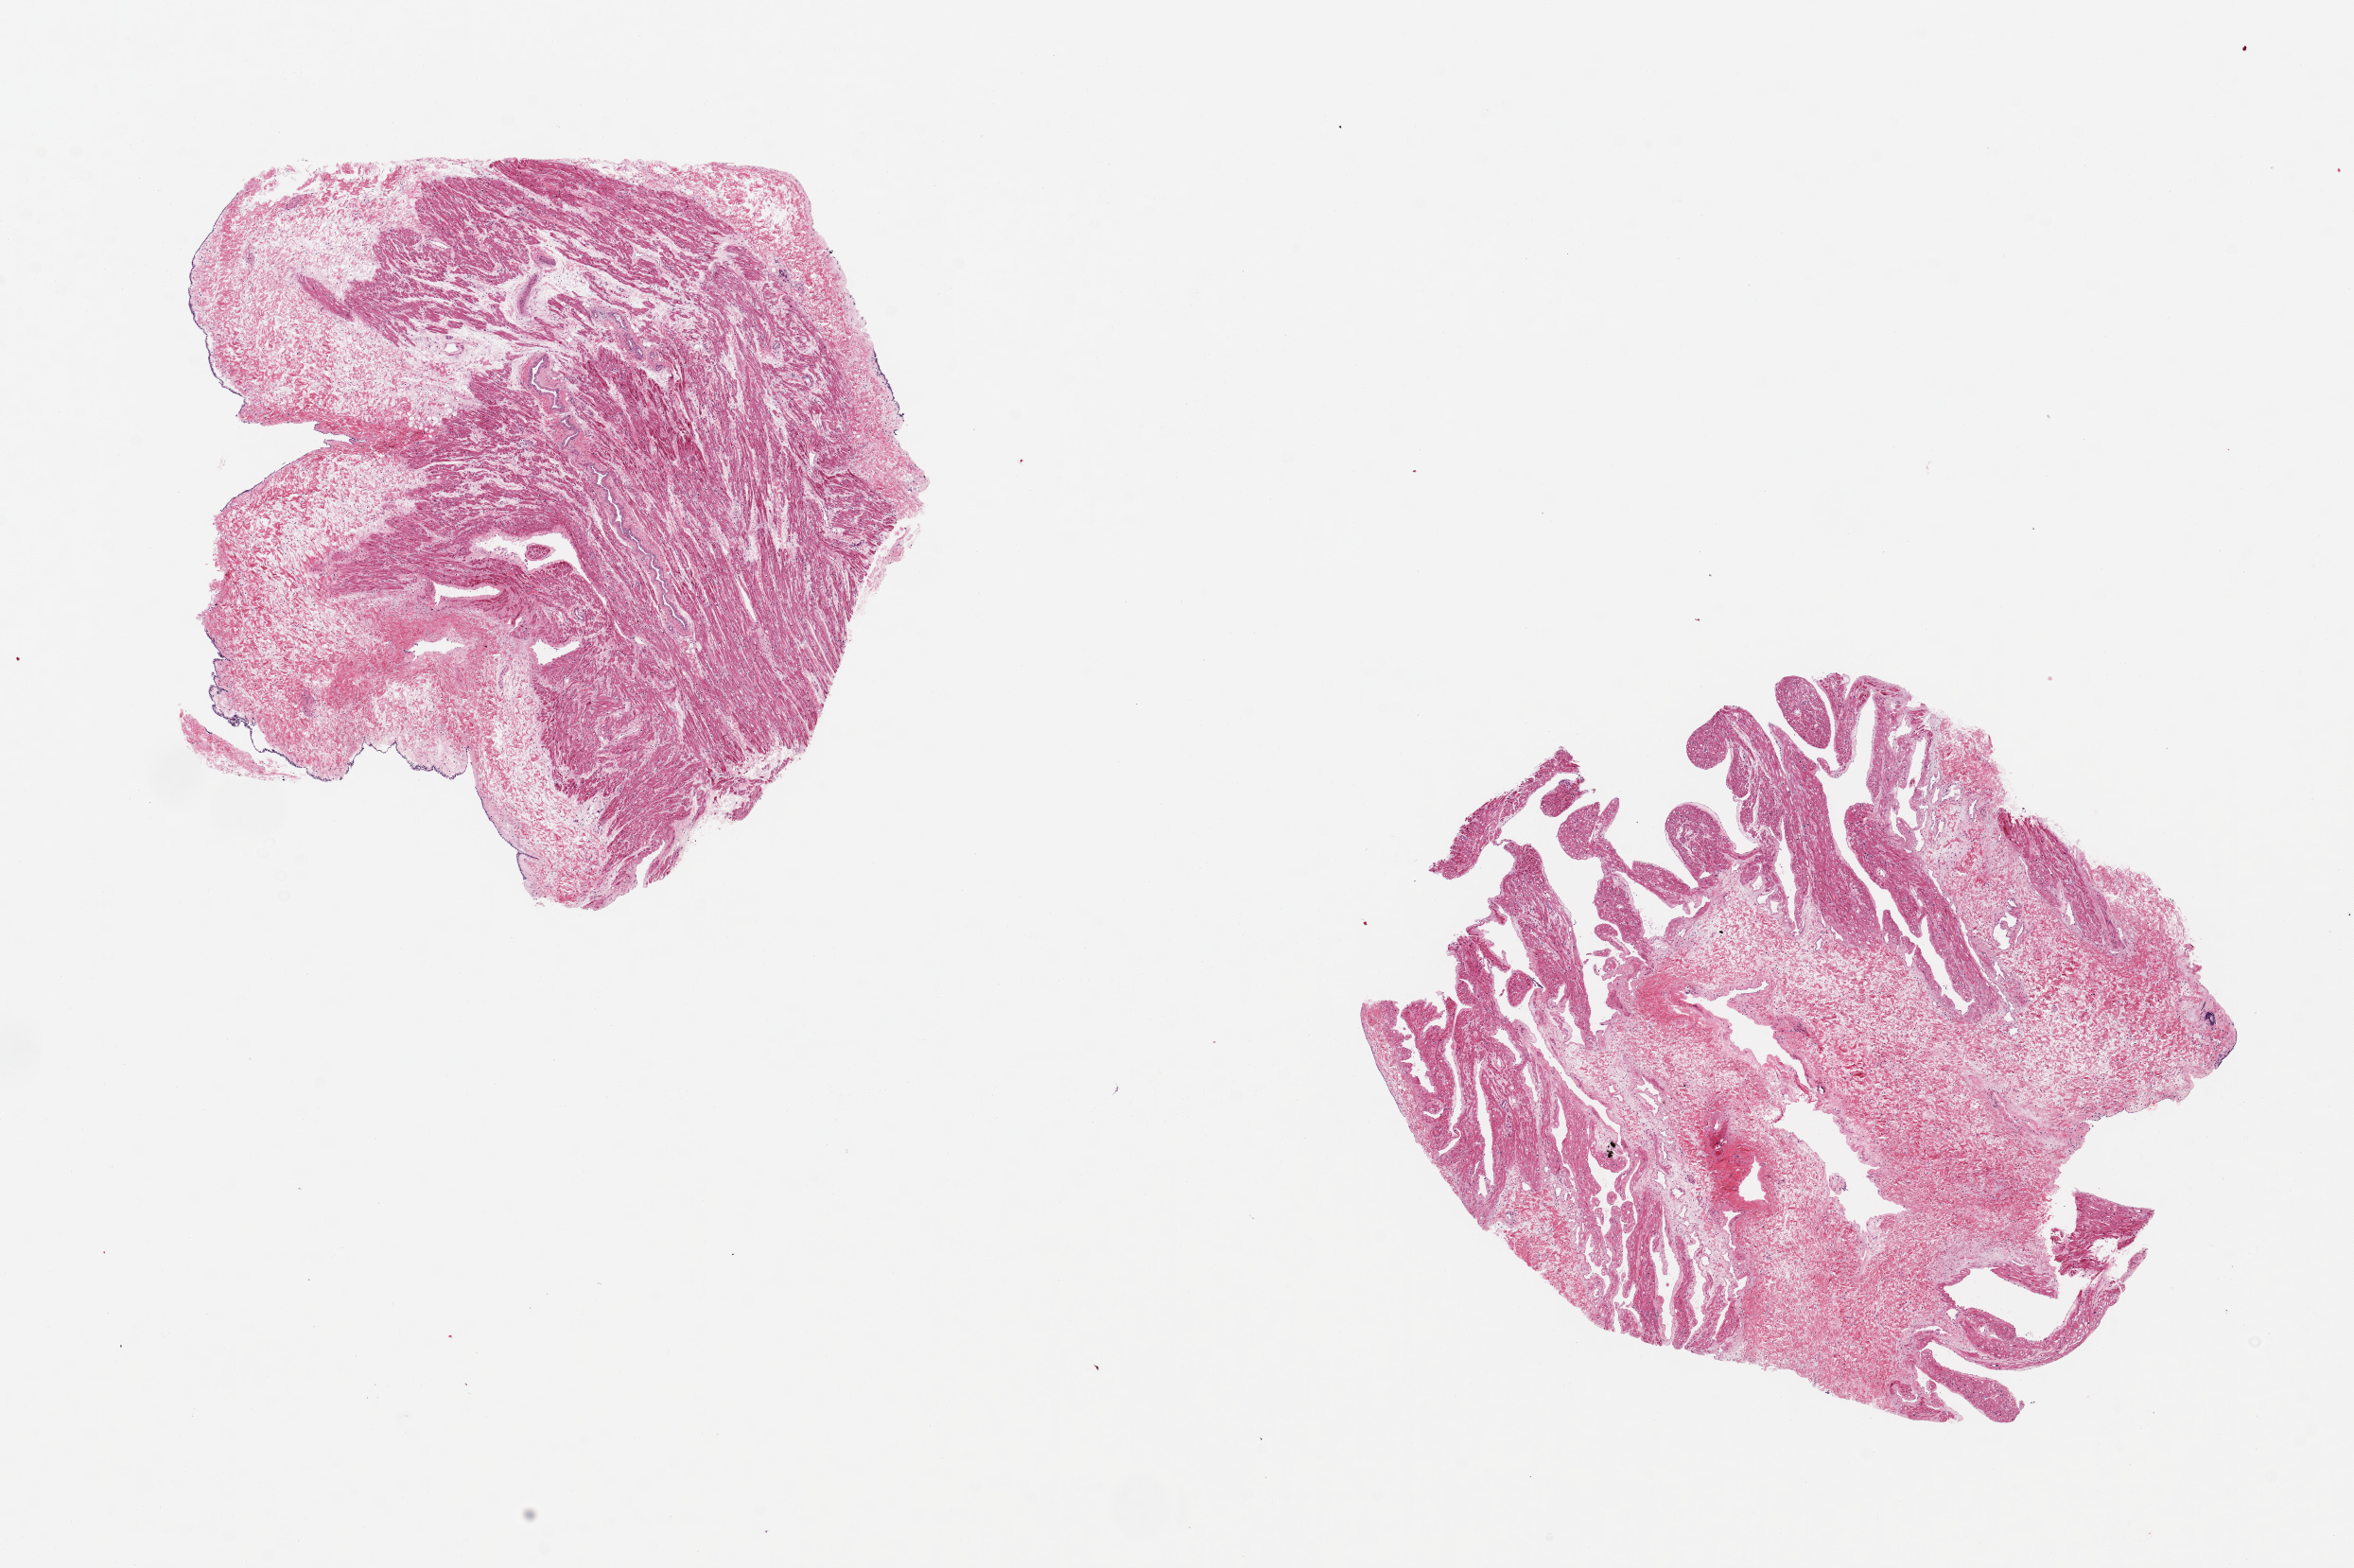
Digitized hematoxylin and eosin (H&E)-stained section — low-resolution overview of the scanned area, about 19.7 x 13.1 mm (slide scanned at 20x). PAXgene-fixed paraffin-embedded (PFPE) section. Sampled site (target tissue): auricular appendage. Tissue donor sample. Donor: male.
Review note (as recorded): 2 pieces, 7x6.5 & 7x6mm; 25 & 60% pericardial stroma, may be due to oblique sectioning.